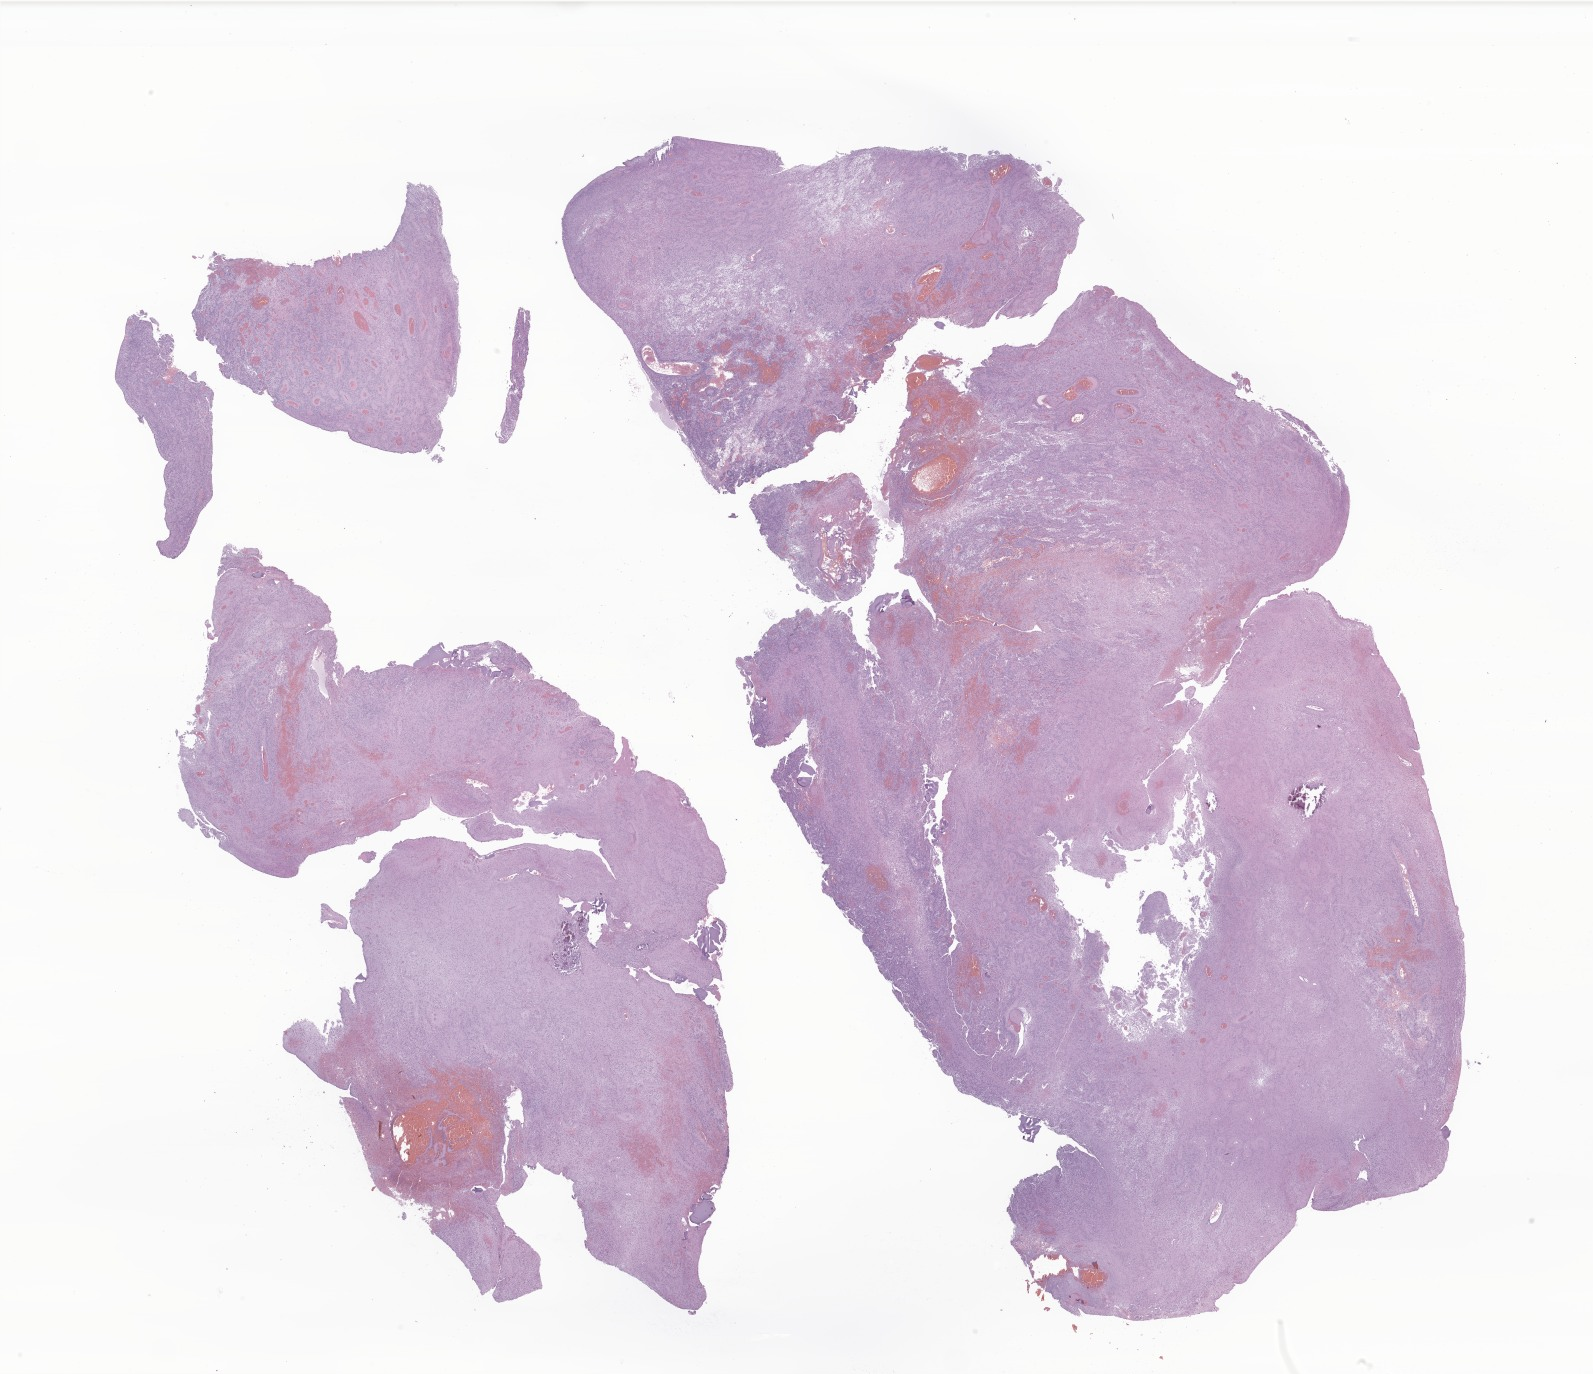
Digitized haematoxylin and eosin-stained section of tumor tissue from the brain — low-resolution overview of the scanned area, about 26.9 x 23.2 mm; FFPE section. Patient male; age 39 months (3 years 3 months).
Diagnosis: Ependymoma, NOS.